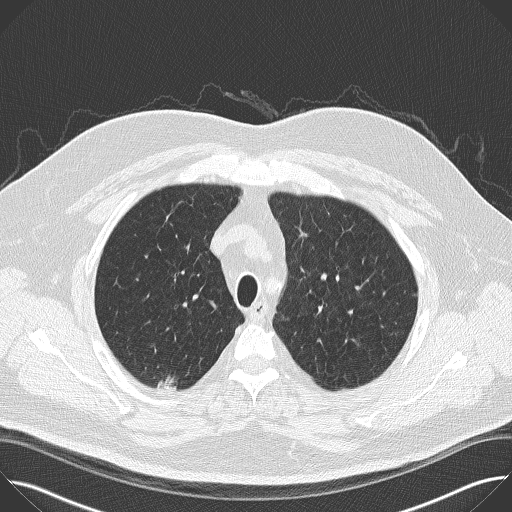
Chest CT (low-dose screening protocol), one axial image, baseline screening round, lung window (W 1500 / L -600 HU), 512 × 512 image matrix. Male participant, aged 65 years at enrolment. Former smoker at enrolment.
Expert-annotated lung lesion, bounding box (x1, y1, x2, y2) in pixels: (143, 366, 191, 403). The screening reader recorded 2 non-calcified nodules or masses ≥4 mm on this exam; which of them this box marks is not recorded. Participant outcome: lung cancer diagnosed 47 days after this screen — bronchiolo-alveolar adenocarcinoma, NOS, right upper lobe, moderately differentiated (G2), stage IIA (AJCC 6th edition), 14 mm at pathology.